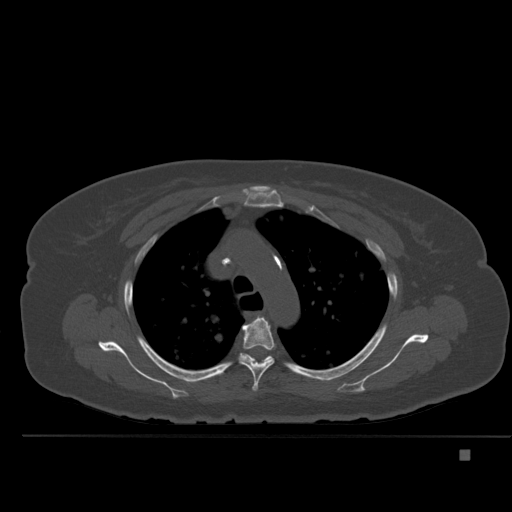
CT including the spine, one axial slice; position 364 of 477 along the scan axis; bone window (W 1800 / L 400 HU); 512 × 512 image matrix, field of view 422 × 422 mm. Female patient, age 74 years. Case-level facts recorded for this patient, not image findings: primary cancer: colon.
Annotated regions visible in this slice (semi-automatically segmented with operator editing):
- T4 vertebra: bounding box <238,318,276,391> (left, top, right, bottom; pixels)
- T5 vertebra: <243,354,273,363>